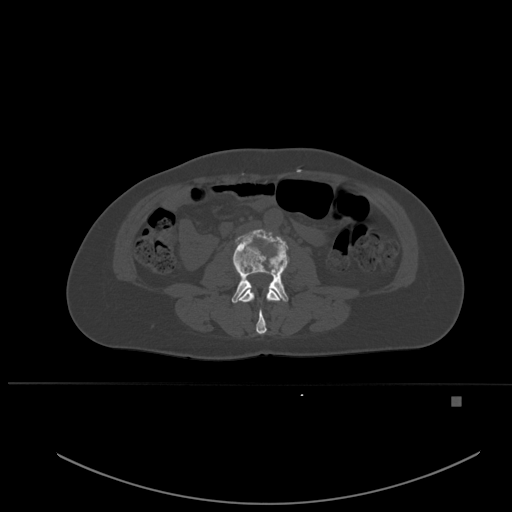
CT including the spine, one axial slice. Position 200 of 651 along the scan axis. Bone window (W 1800 / L 400 HU). 1.5 mm slice thickness. 512 × 512 image matrix, field of view 443 × 443 mm. Patient: female, 49 years. From the clinical record (not read from this slice): primary cancer: breast; vertebrae with lytic lesions (as recorded): L3, T12, L4.
Structures marked on this image (semi-automatically segmented with operator editing):
- L2 vertebra: bounding box [x1, y1, x2, y2] px = [239, 289, 281, 335]
- L3 vertebra: [231, 231, 288, 303]